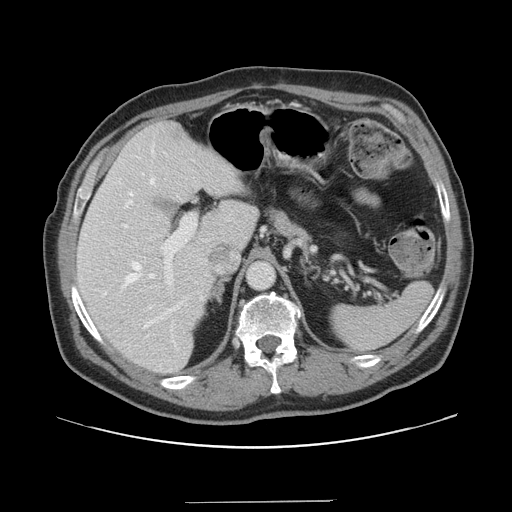
Contrast-enhanced abdominal CT, one axial slice. Slice 100 of 151 in the series (ordered by position). 120 kVp. Intravenous contrast given. Soft-tissue window (W 400 / L 40 HU). 512 × 512 image matrix, field of view 399 × 399 mm. Male patient, age 63 years. Case-level facts recorded for this patient, not image findings: diagnosis: colorectal cancer liver metastases, imaged before liver resection; multiple liver metastases: no; largest metastasis: 2.1 cm; disease in both lobes: no.
Structures marked on this image (expert manual segmentation):
- hepatic veins: bounding box (x1, y1, x2, y2) in pixels: (105, 149, 188, 350)
- liver: (78, 122, 258, 373)
- planned liver remnant (the part of the liver to remain after resection): (78, 122, 257, 373)
- portal vein (with intrahepatic branches): (148, 214, 197, 309)